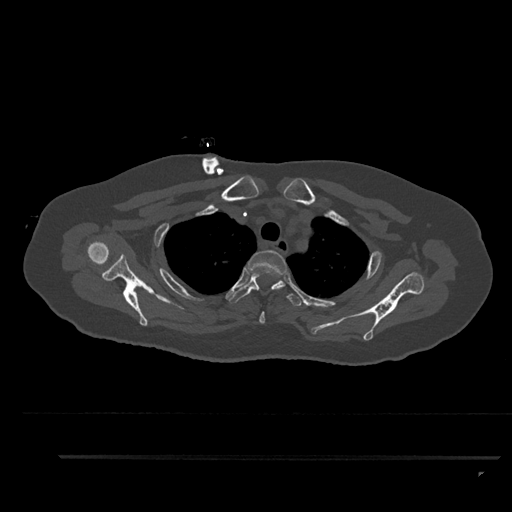
CT including the spine, one axial slice; slice 701 of 797 in the series (ordered by position); reconstruction kernel Br40s/3; bone window (W 1800 / L 400 HU); 0.5 mm slice thickness; 512 × 512 image matrix, field of view 408 × 408 mm. Female patient, age 44 years. Case-level facts recorded for this patient, not image findings: primary cancer: renal; vertebrae with lytic lesions (as recorded): L1.
Structures marked on this image (semi-automatic segmentation, software-assisted and operator-edited):
- T2 vertebra: bounding box (x1, y1, x2, y2) in pixels: (248, 250, 287, 324)
- T3 vertebra: (228, 272, 304, 306)